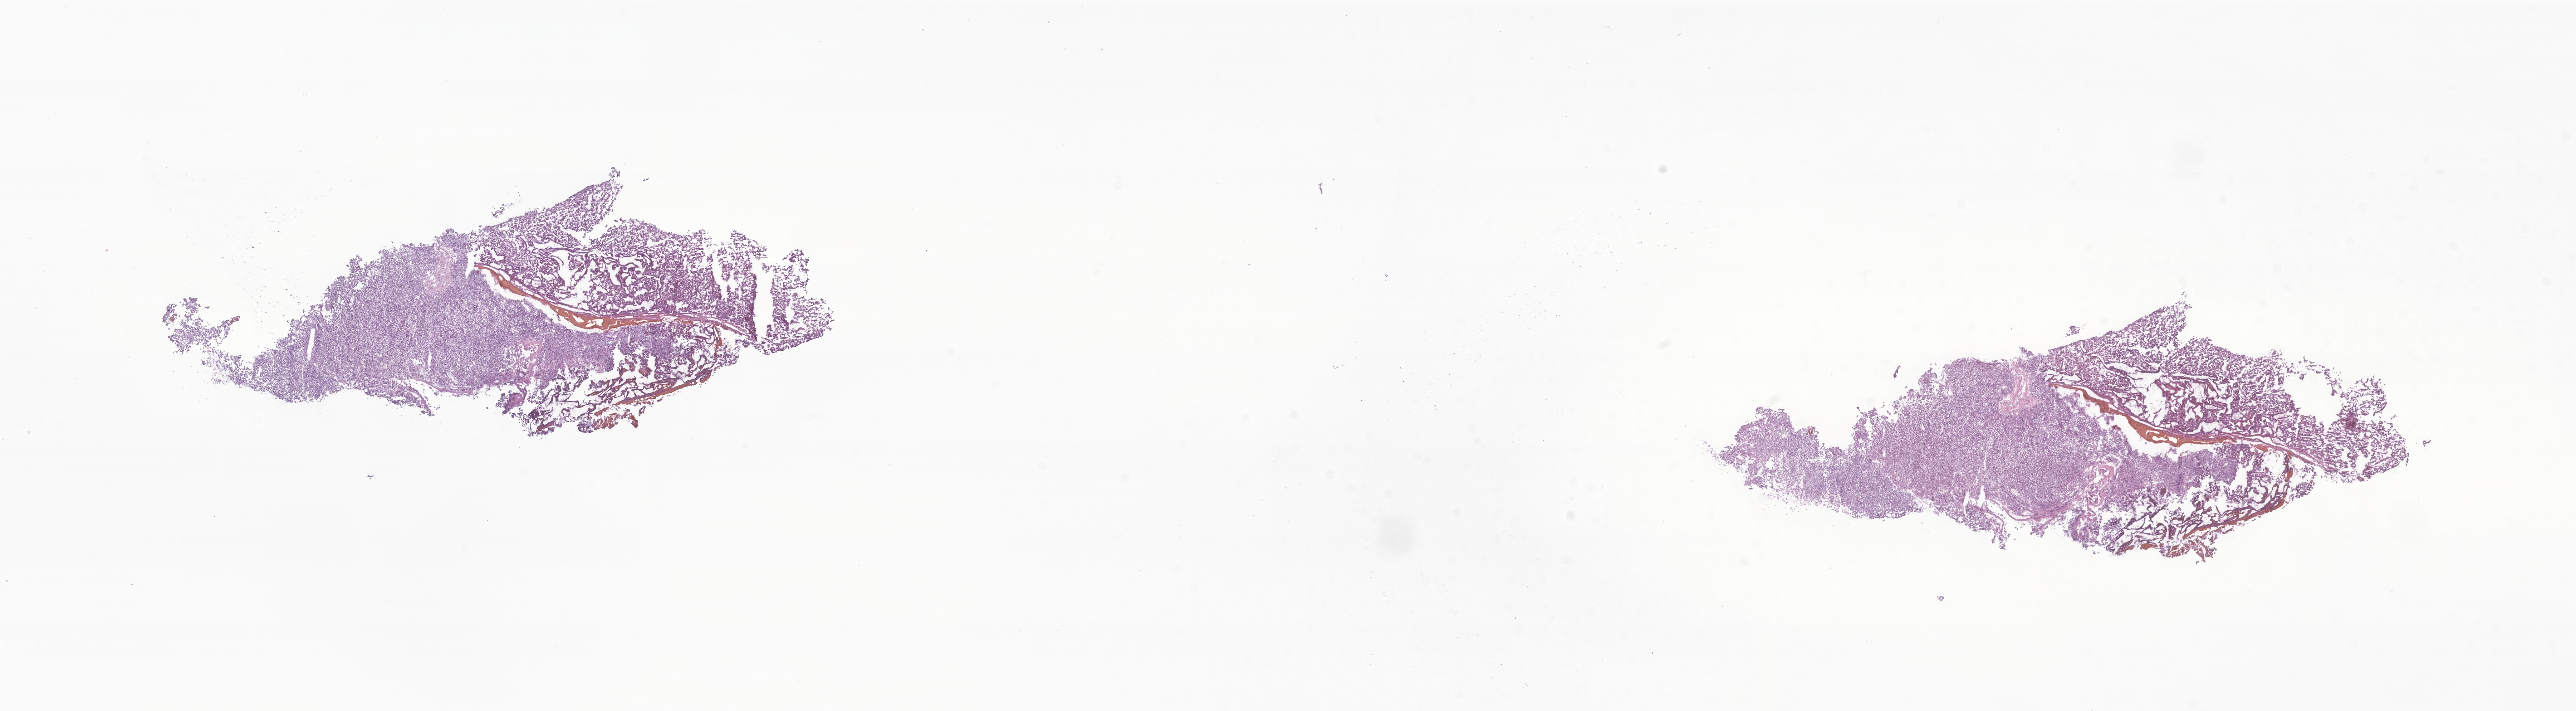
Digitized haematoxylin and eosin-stained section of tumor tissue from the occipital lobe — a low-resolution overview of the entire scanned area, about 30.4 x 8.4 mm; frozen section (OCT-embedded). Patient female; age 105 months (8 years 9 months).
- diagnosis (ICD-O-3 morphology term): Glioma, malignant